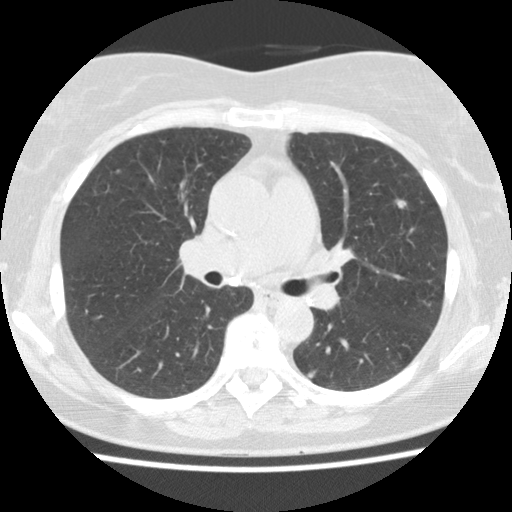
Chest CT (low-dose screening protocol), one axial image; first (baseline) screen; lung window (W 1500 / L -600 HU); standard (soft-tissue) reconstruction kernel (STANDARD); slice 53 of 123 in the series; 512 × 512 image matrix, field of view 310 × 310 mm. Female participant, aged 60 years at enrolment. Current smoker at enrolment.
- Lesion marked by an expert reader, box from (x=376, y=189) to (x=421, y=225) px.
- The screening reader recorded 2 non-calcified nodules or masses ≥4 mm on this exam (left upper lobe, right upper lobe); which of them this box marks is not recorded.
- Official screen result: positive, change unspecified: nodule(s) >= 4 mm or enlarging nodule(s), mass(es), or other non-specific abnormalities suspicious for lung cancer.
- Later outcome: lung cancer diagnosed 388 days after this screen (after the second annual screen) — non-small cell carcinoma, left upper lobe, poorly differentiated (G3), stage IA (AJCC 6th edition), 10 mm at pathology.